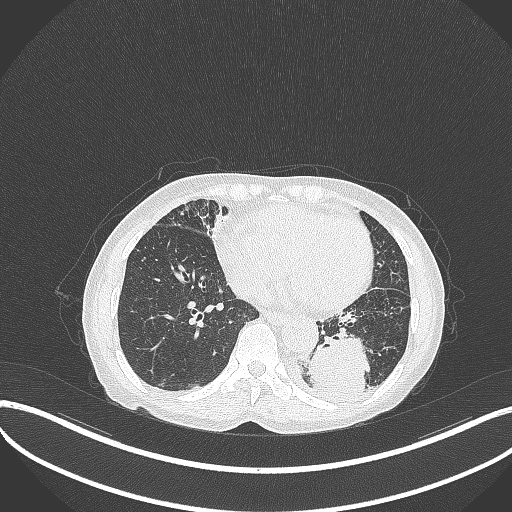
Chest CT, one axial slice; slice 100 of 370 in the series (ordered by position); reconstruction kernel B70f; 120 kVp; lung window (W 1500 / L -600 HU); 1 mm slice thickness; 512 × 512 image matrix, field of view 400 × 400 mm. Female patient, age 78 years. Case-level facts recorded for this patient, not image findings: clinical TNM (as recorded): T3 N0 M1.
Structures marked on this image (bounding box drawn by a radiologist):
- lung tumour (recorded histology: squamous cell carcinoma): bounding box (x1, y1, x2, y2) in pixels: (308, 333, 375, 400)